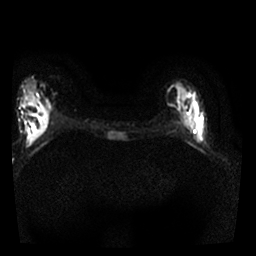
Breast MRI, one axial slice. Position 8 of 25 along the scan axis. Diffusion-weighted series; image 2 of 4 stored at this slice position (different b-values; order by instance number). 1.5 T. 4 mm slice thickness. 256 × 256 image matrix, field of view 300 × 300 mm. Female patient.
Structures marked on this image (manually delineated by an expert):
- tumour on diffusion-weighted imaging: bounding box (x1, y1, x2, y2) in pixels: (187, 115, 205, 144)